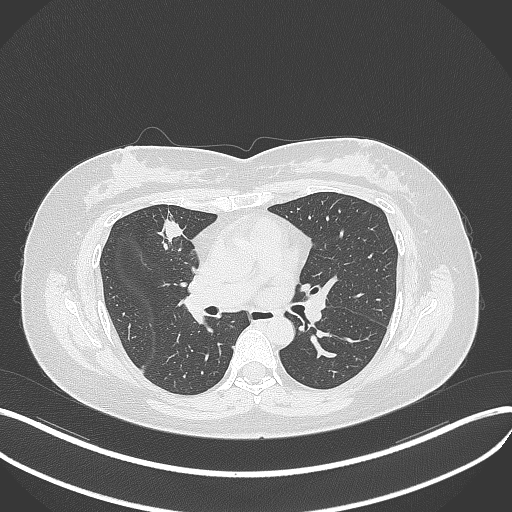
Chest CT, one axial slice; slice 174 of 273 in the series (ordered by position); reconstruction kernel B70f; 120 kVp; lung window (W 1500 / L -600 HU); 1 mm slice thickness; 512 × 512 image matrix. Patient: female, 42 years. From the clinical record (not read from this slice): clinical TNM (as recorded): T1b N0 M0.
Structures marked on this image (rectangle marked by the reading radiologist):
- lung tumour (recorded histology: adenocarcinoma): box from (x=155, y=210) to (x=186, y=250) px